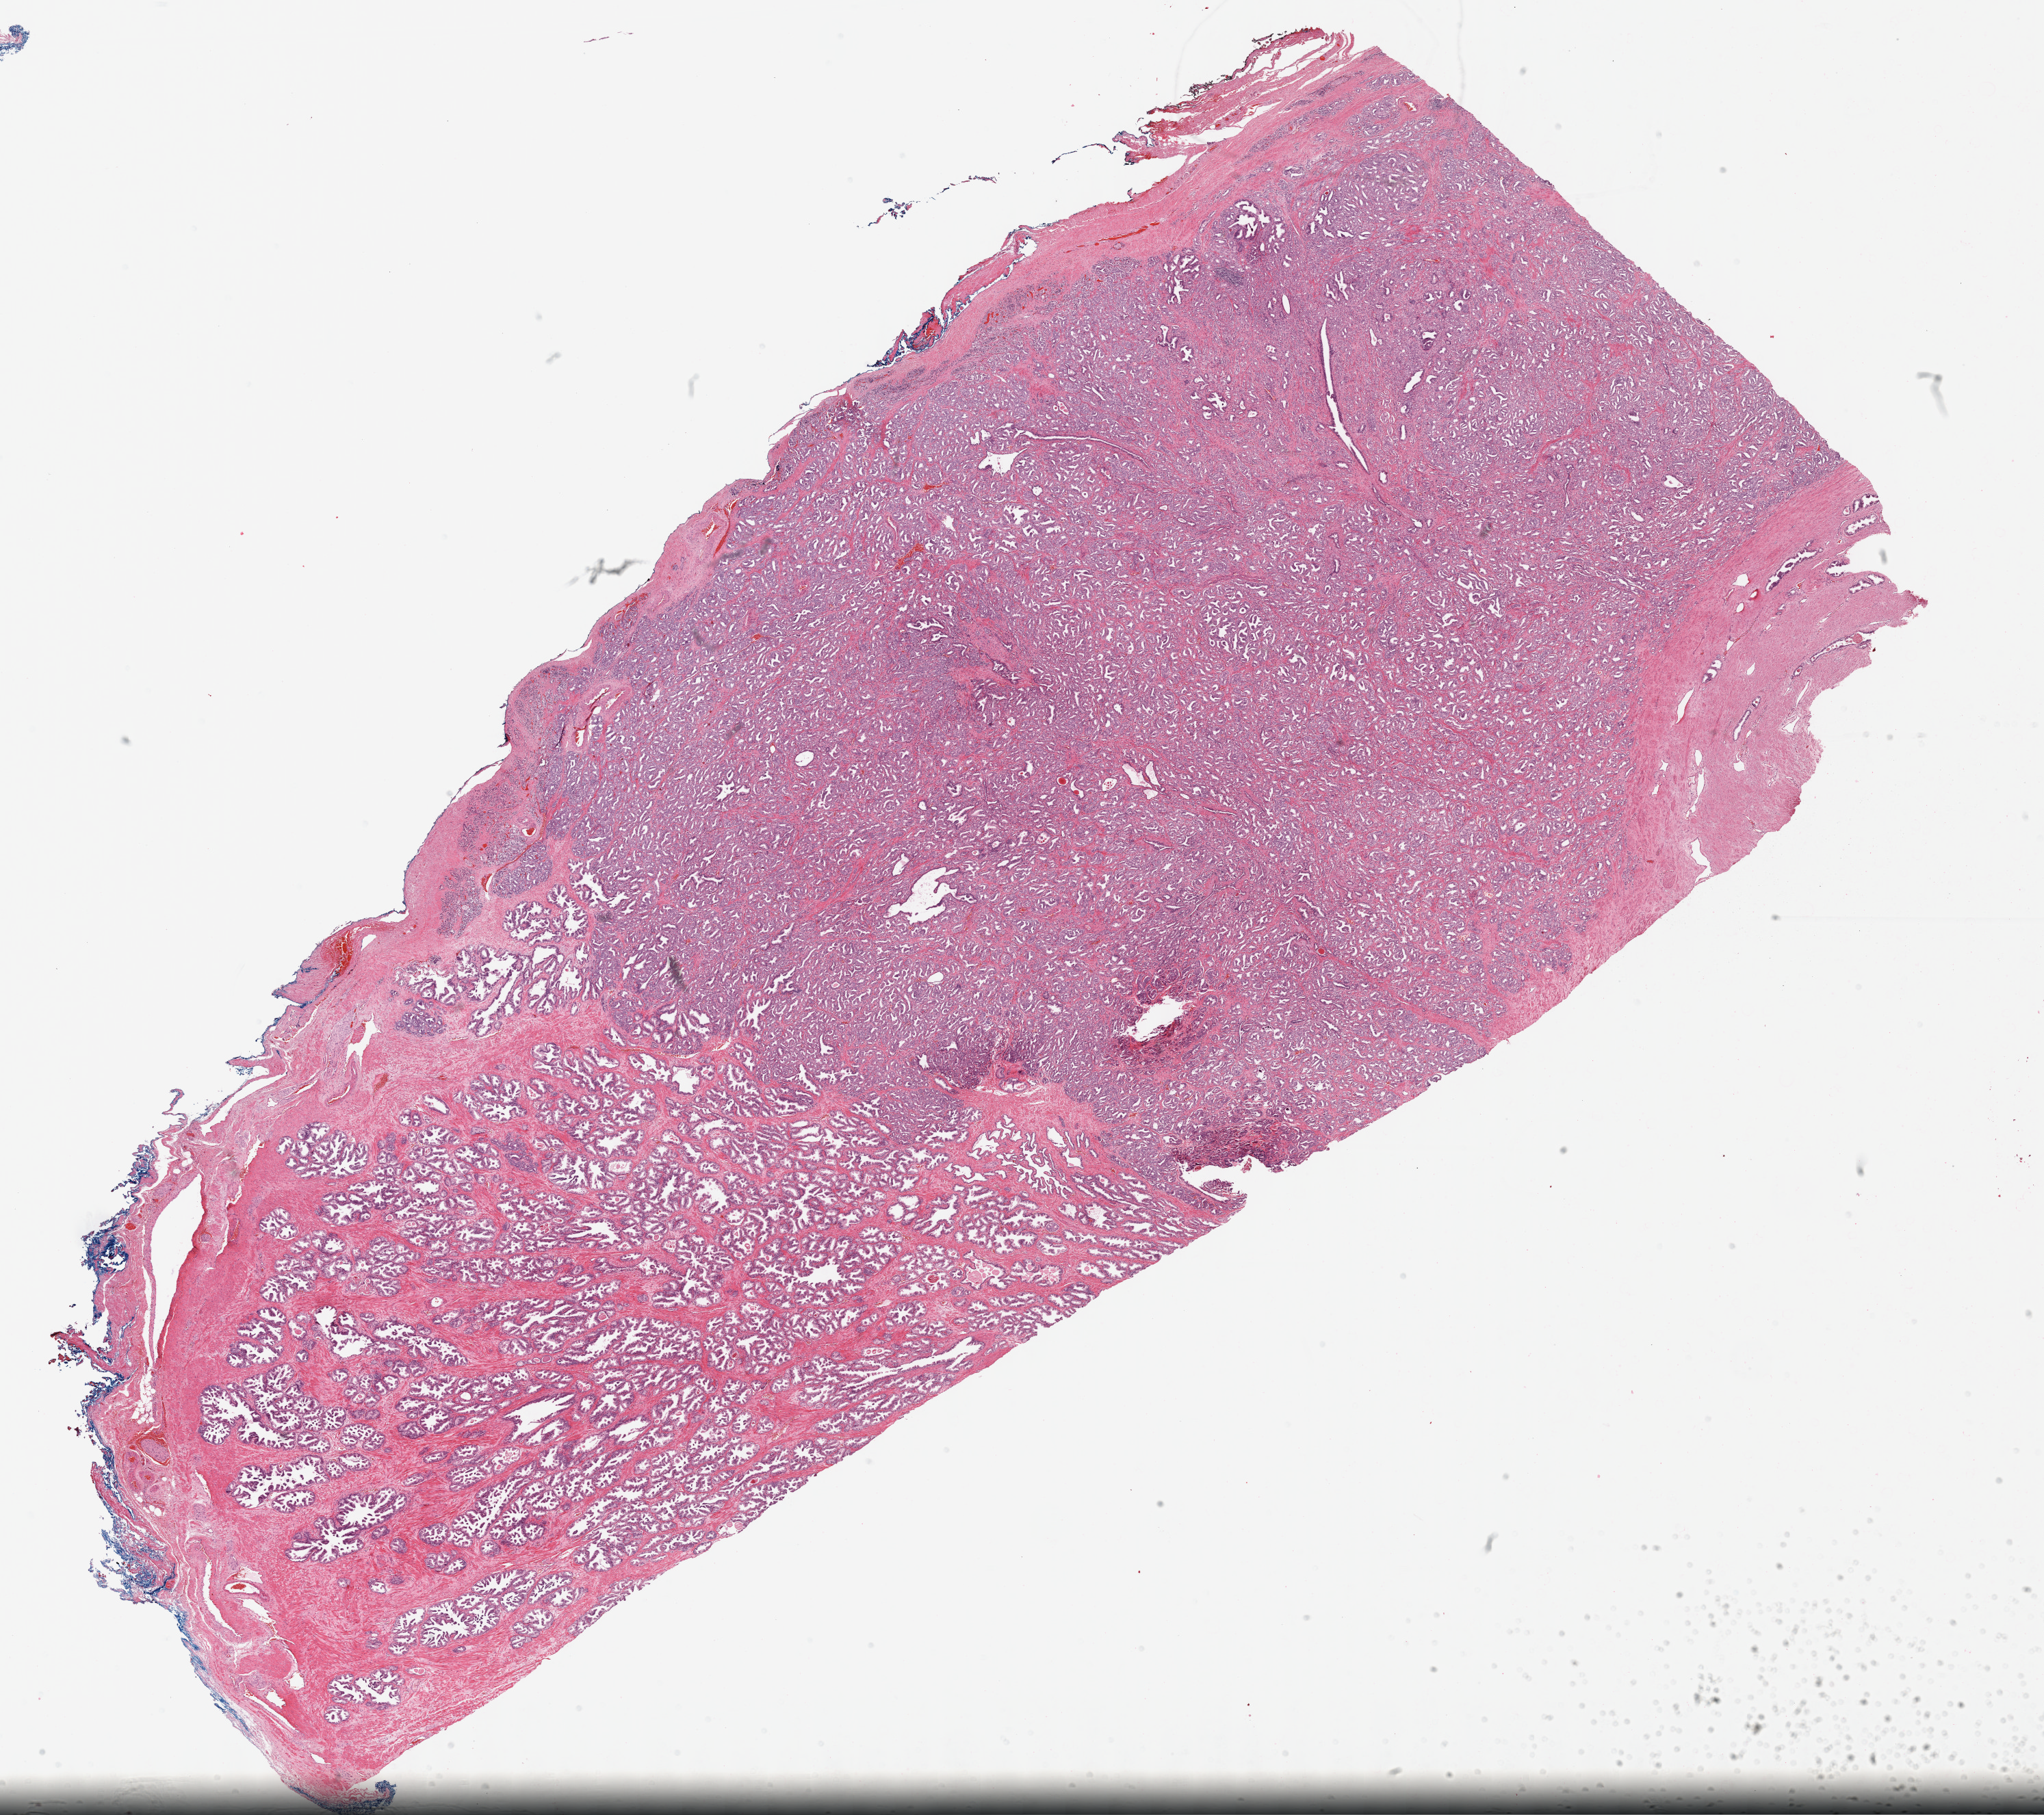
H&E-stained whole-slide image — low-resolution overview of the scanned area, about 24.2 x 21.5 mm, formalin-fixed paraffin-embedded (FFPE) diagnostic section, sample: primary tumour, prostate. Male patient; age at initial diagnosis 66 years. Gleason score: 9 (4+5).
Pathologic diagnosis: Adenocarcinoma, NOS (prostate gland).